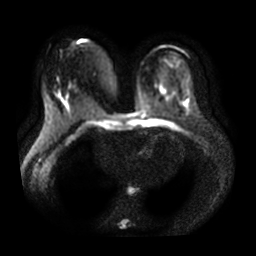
Breast MRI, one axial slice; position 19 of 35 along the scan axis; diffusion-weighted series; image 2 of 4 stored at this slice position (different b-values; order by instance number); 3 T; 256 × 256 image matrix, field of view 360 × 360 mm. Female patient.
Annotated regions visible in this slice (expert manual segmentation):
- tumour on diffusion-weighted imaging: bounding box (x1, y1, x2, y2) in pixels: (64, 101, 69, 109)